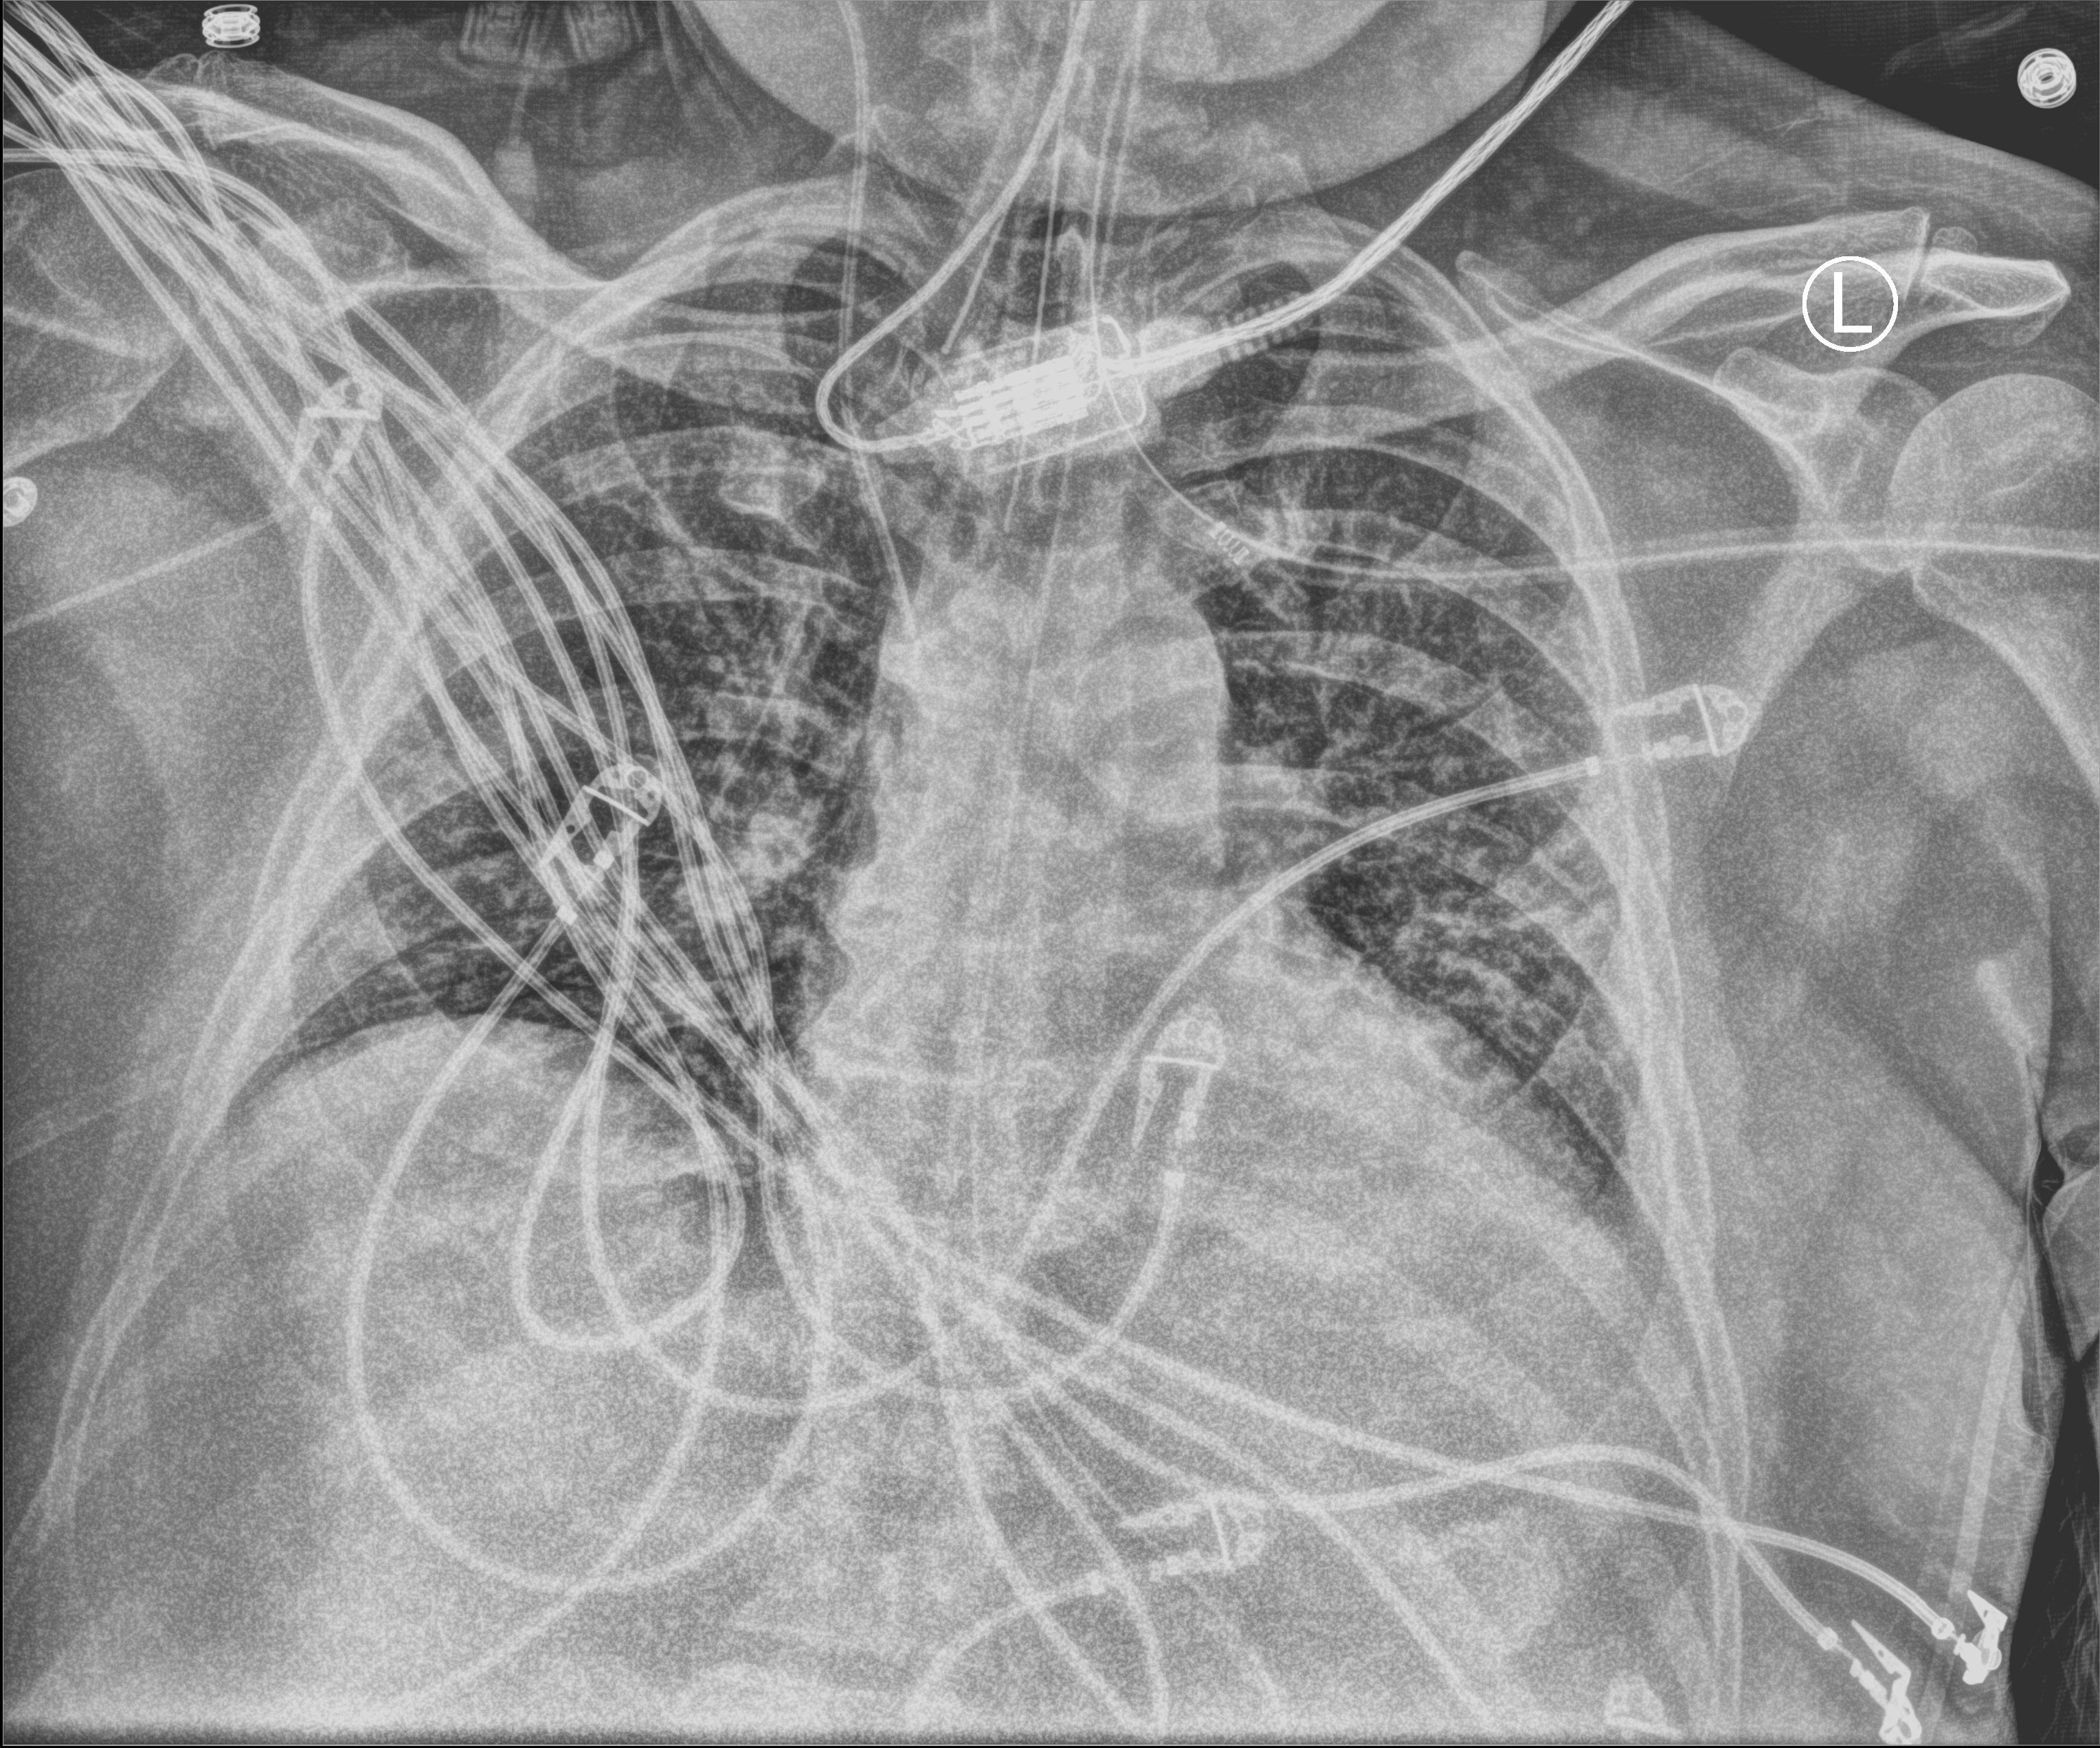
Portable chest radiograph; anteroposterior (AP) projection. Patient hospitalised with COVID-19; male, aged 18–59 years.
Hospital-stay facts (about this admission, not read from this image; timing relative to this image not recorded): chronic kidney disease (admission record): no; admitted to intensive care during this hospital stay: yes.